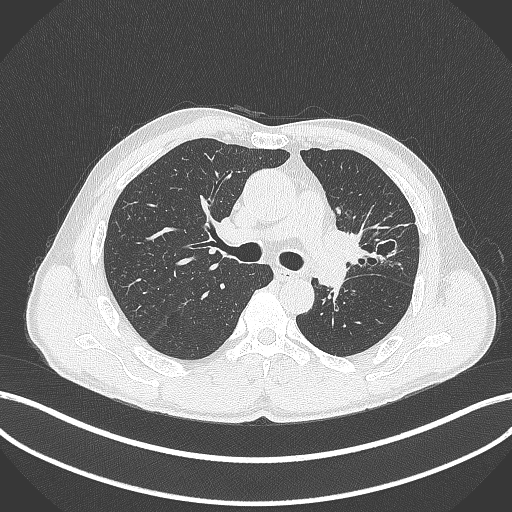
Chest CT, one axial slice; position 263 of 429 along the scan axis; reconstruction kernel B70f; lung window (W 1500 / L -600 HU); 1 mm slice thickness; 512 × 512 image matrix, field of view 400 × 400 mm. Patient: male, 57 years. Case-level facts recorded for this patient, not image findings: clinical TNM (as recorded): T2b N0 M0.
Outlined on this slice (rectangle marked by the reading radiologist):
- lung tumour (recorded histology: squamous cell carcinoma): box from (x=319, y=225) to (x=380, y=272) px